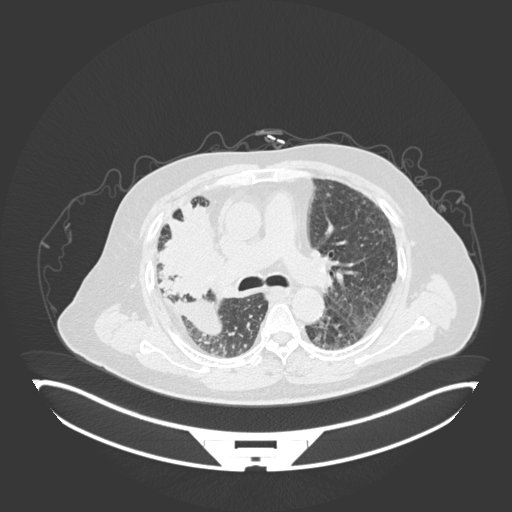
Chest CT, one axial slice; slice 105 of 201 in the series (ordered by position); reconstruction kernel B30f; lung window (W 1500 / L -600 HU); 1 mm slice thickness; 512 × 512 image matrix, field of view 500 × 500 mm. Patient: male, 69 years. Case-level facts recorded for this patient, not image findings: clinical TNM (as recorded): T4 N3 M1.
Structures marked on this image (bounding box drawn by a radiologist):
- lung tumour (recorded histology: adenocarcinoma): bounding box <158,197,226,296> (left, top, right, bottom; pixels)